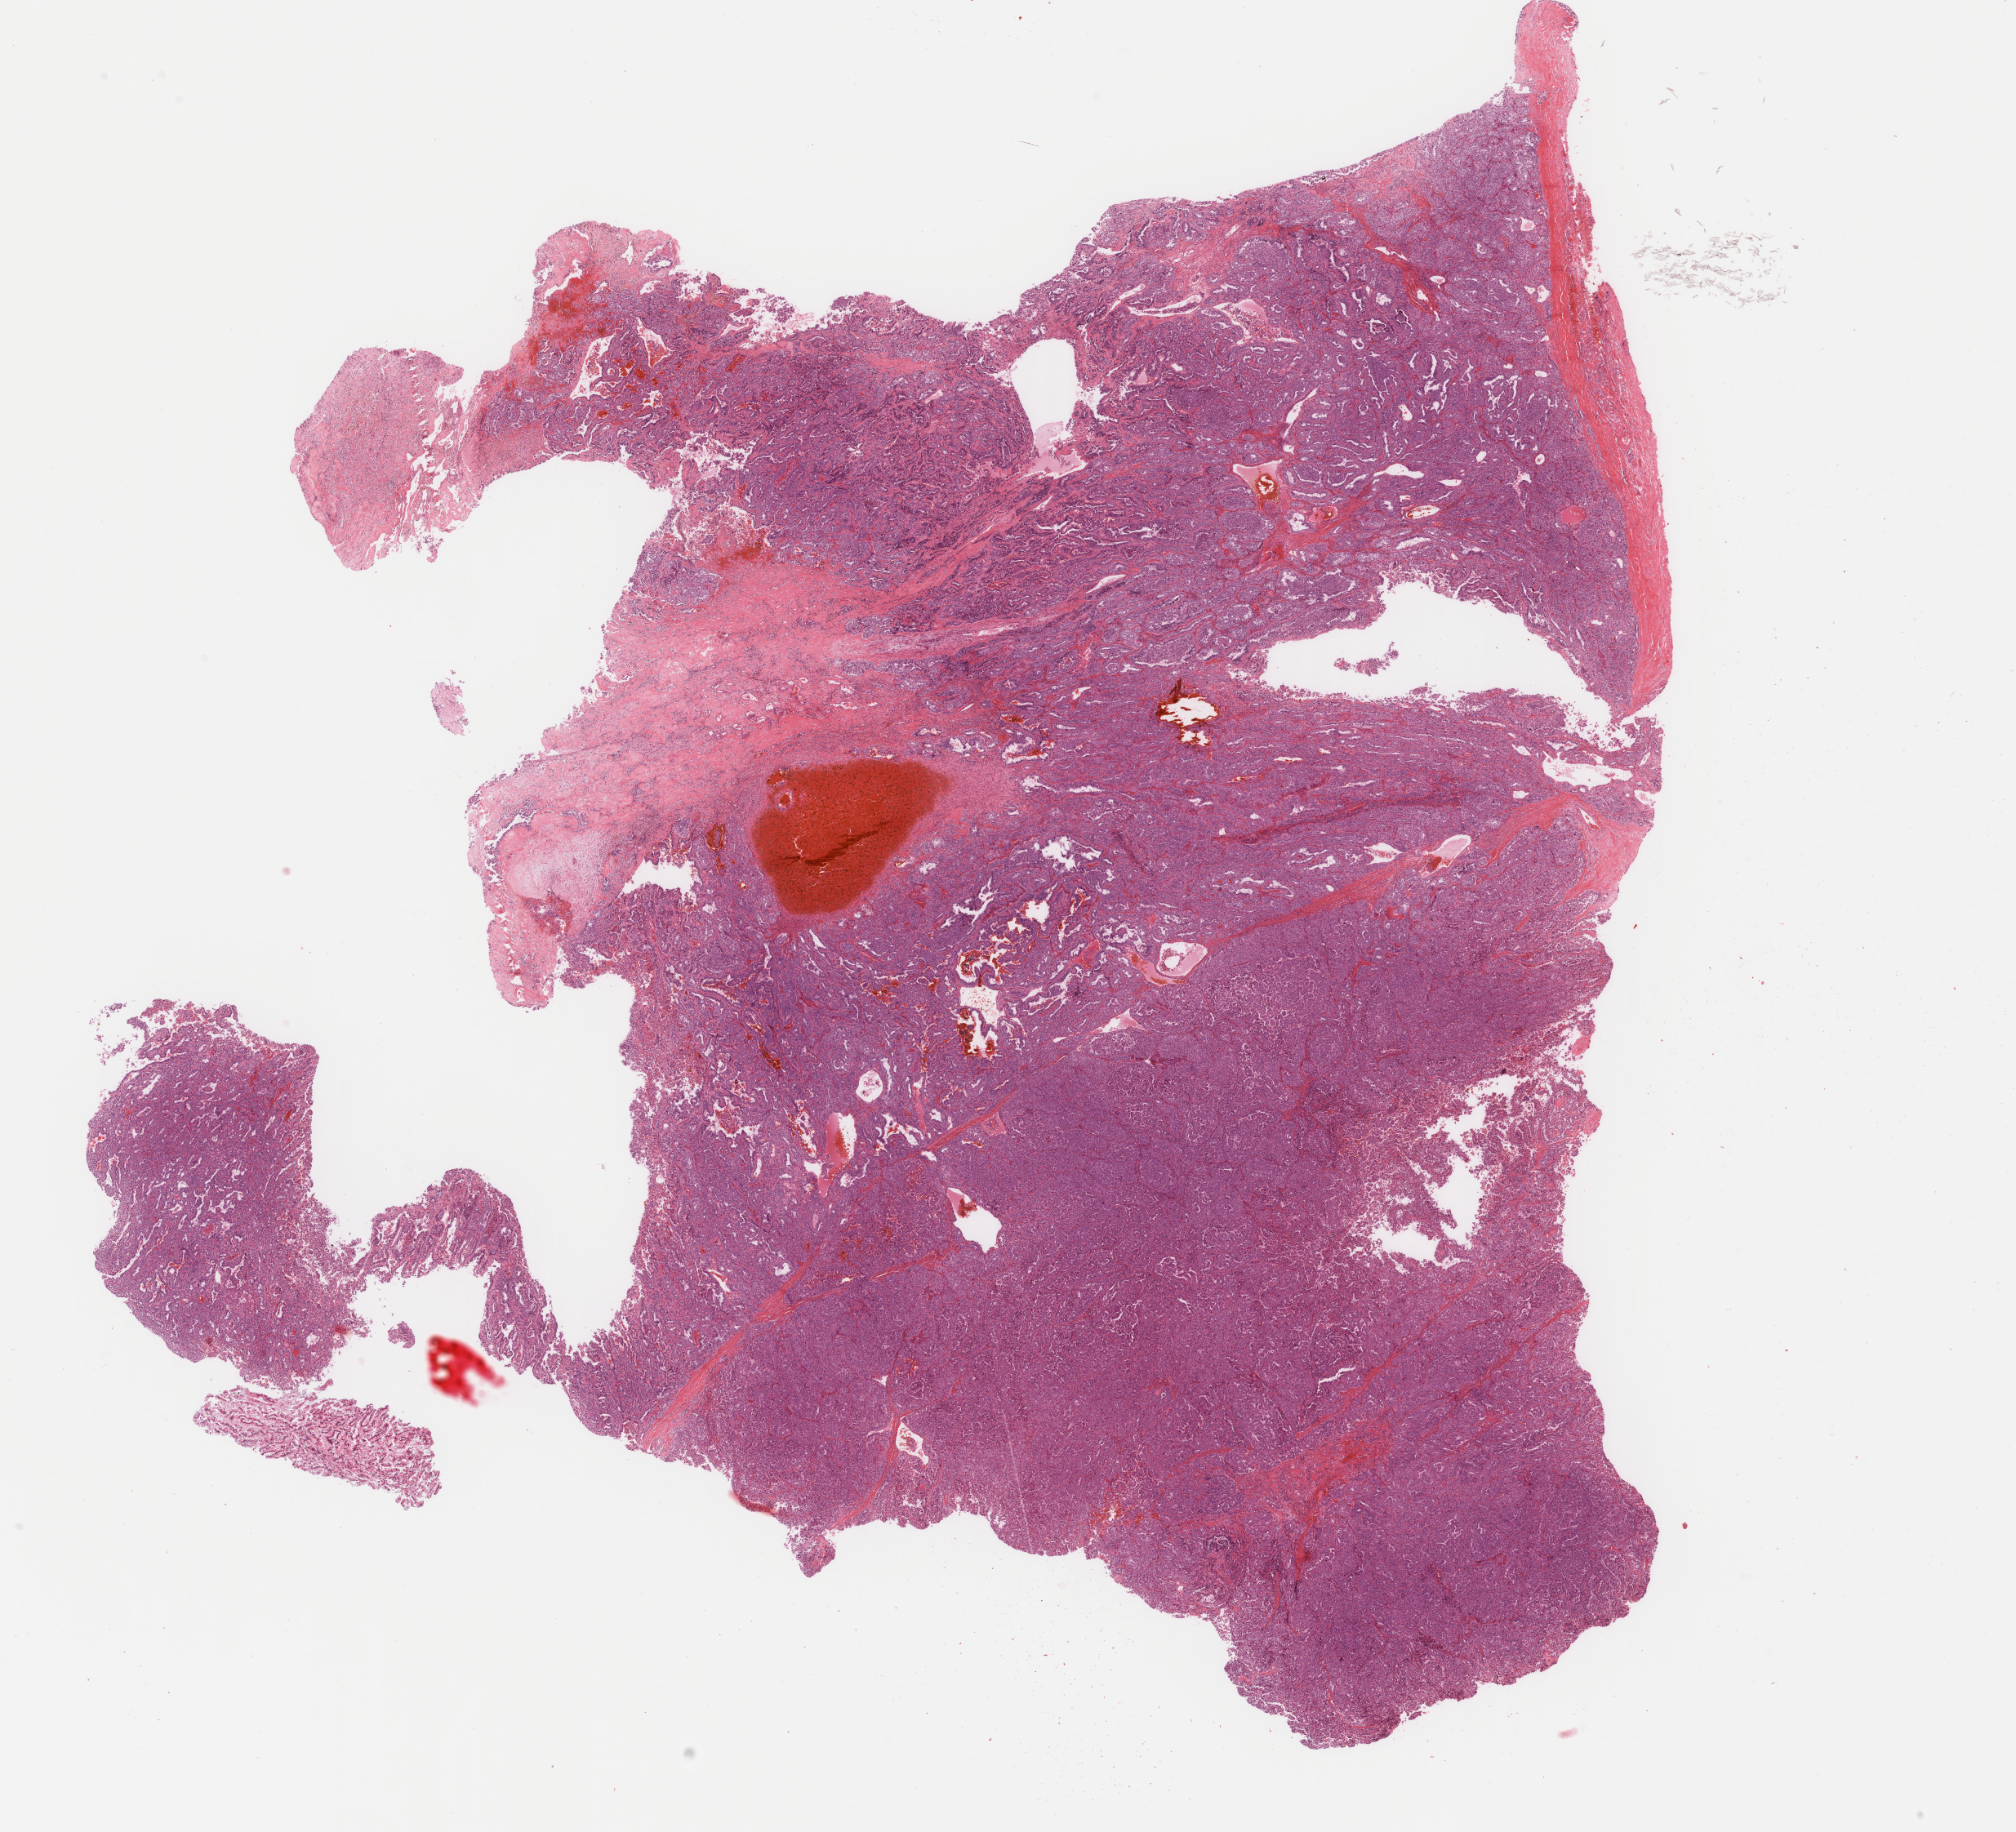
Whole-slide histology image, H&E-stained, a low-resolution overview of the entire scanned area, about 19.6 x 17.8 mm; FFPE section; primary tumour sample from the thyroid. Patient: female, age at initial diagnosis 57 years.
Pathologic diagnosis: Papillary adenocarcinoma, NOS (thyroid gland). AJCC pathologic stage: II.